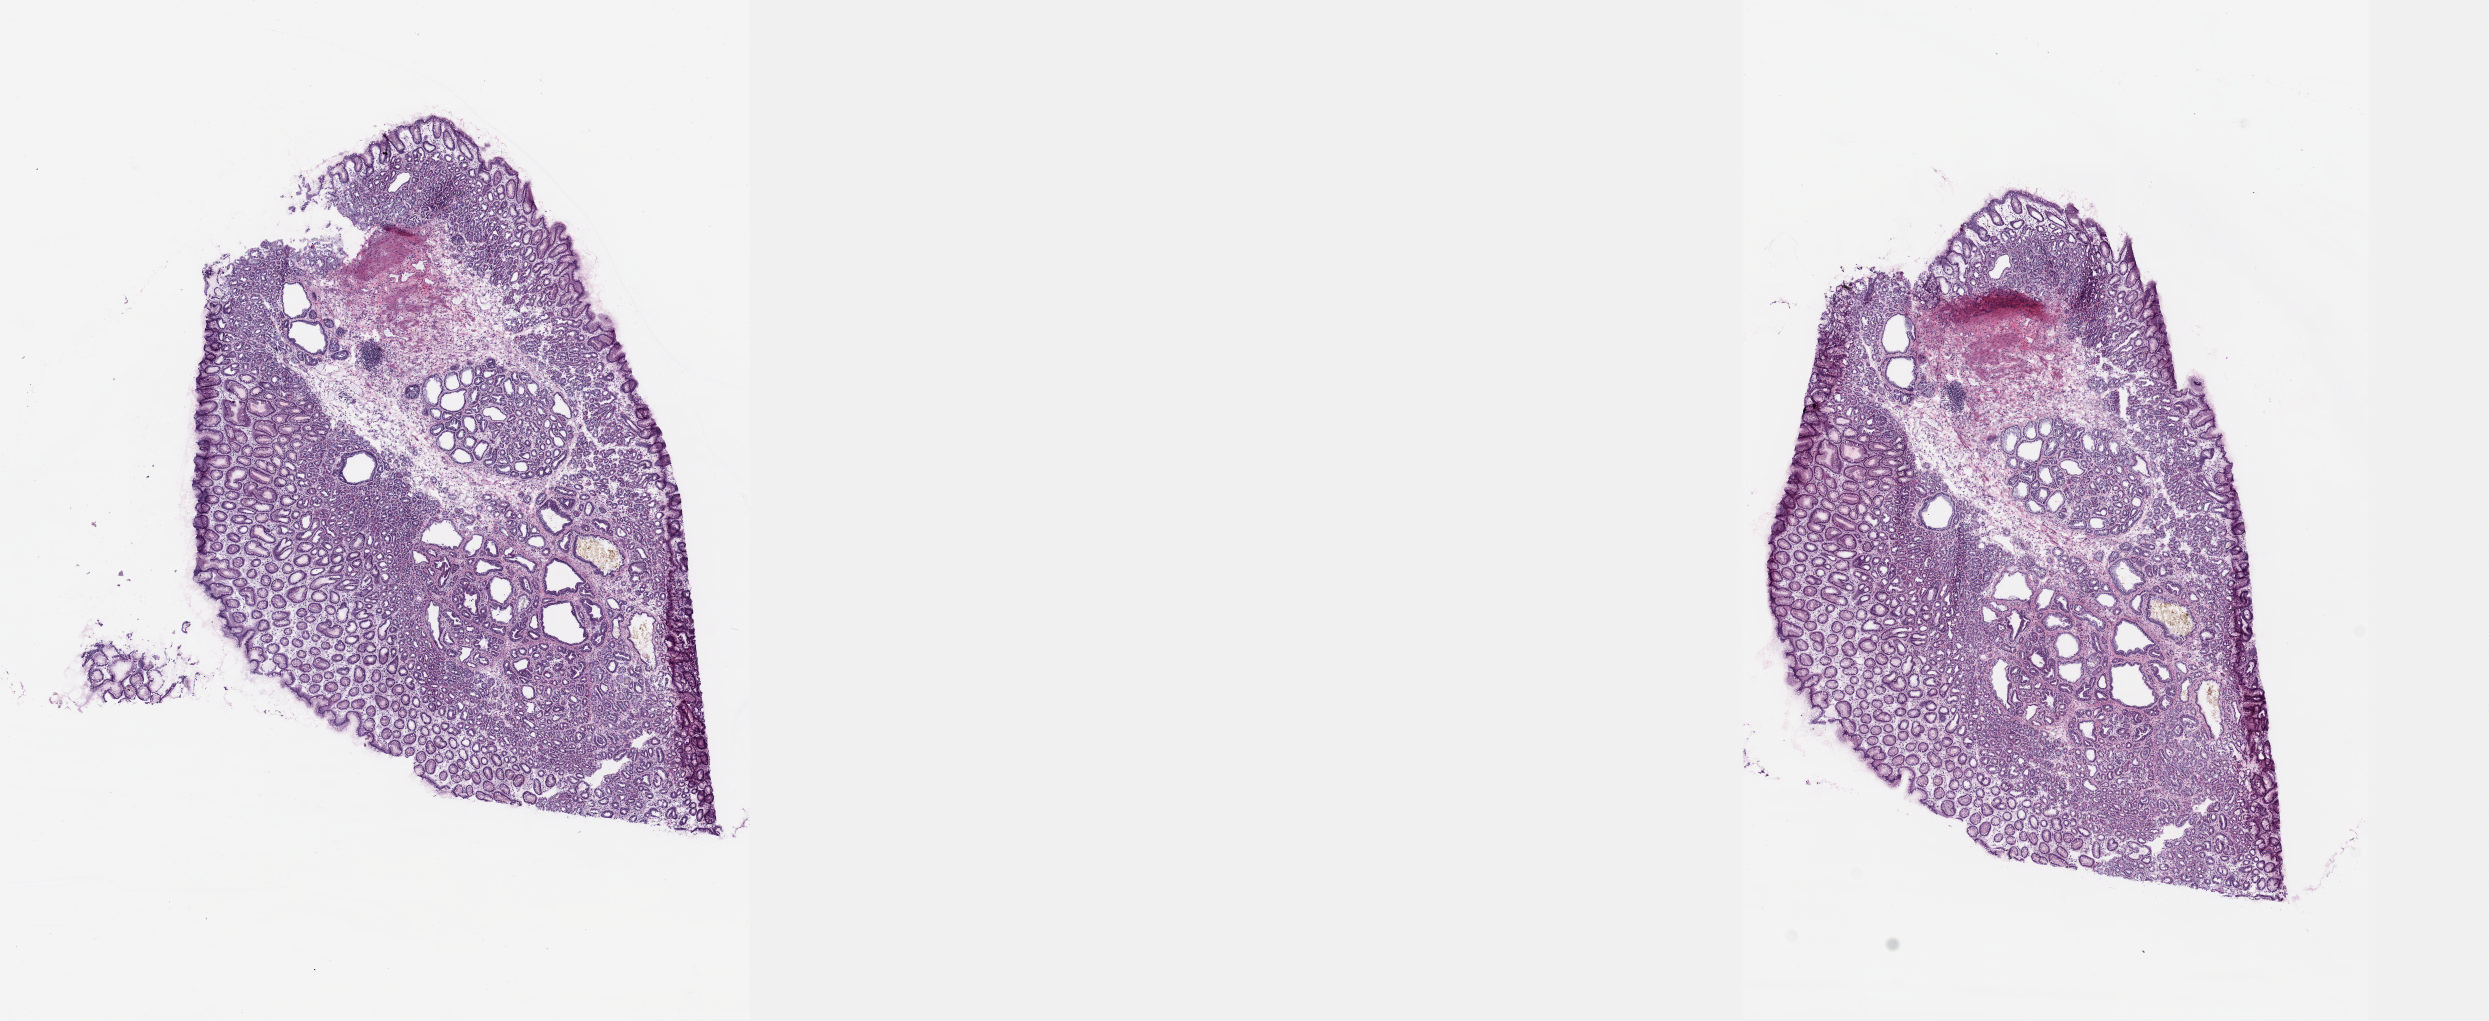
Whole-slide histology image, H&E-stained — shown as a low-resolution overview of the whole scanned area (about 20.1 x 8.2 mm, slide scanned at 20x), frozen section, sample: solid tissue normal (non-tumour tissue), esophagus. Male patient; age at initial diagnosis 76 years. Pathologist review of this section (percent, as recorded): tumour cells 0%, tumour nuclei 0%, normal cells 100%, stromal cells 0%, necrosis 0%. Inflammatory infiltration, as recorded: lymphocyte infiltration 5%, monocyte infiltration 0%, neutrophil infiltration 0%.
* this section: solid tissue normal (non-tumour) sample from the same patient
* patient diagnosis: Adenocarcinoma, NOS (lower third of esophagus)